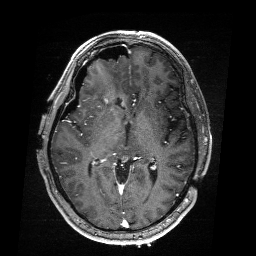
Brain MRI from a brain-tumour surgery series, one axial slice. Position 108 of 176 along the scan axis. T1-weighted post-contrast. 256 × 256 image matrix, field of view 256 × 256 mm. Case-level facts recorded for this patient, not image findings: histopathology: Astrocytoma; WHO grade: 4; IDH mutation: yes; tumour location: Right Frontal.
Structures marked on this image (manually delineated by an expert):
- residual tumour: bounding box [x1, y1, x2, y2] px = [104, 90, 110, 96]